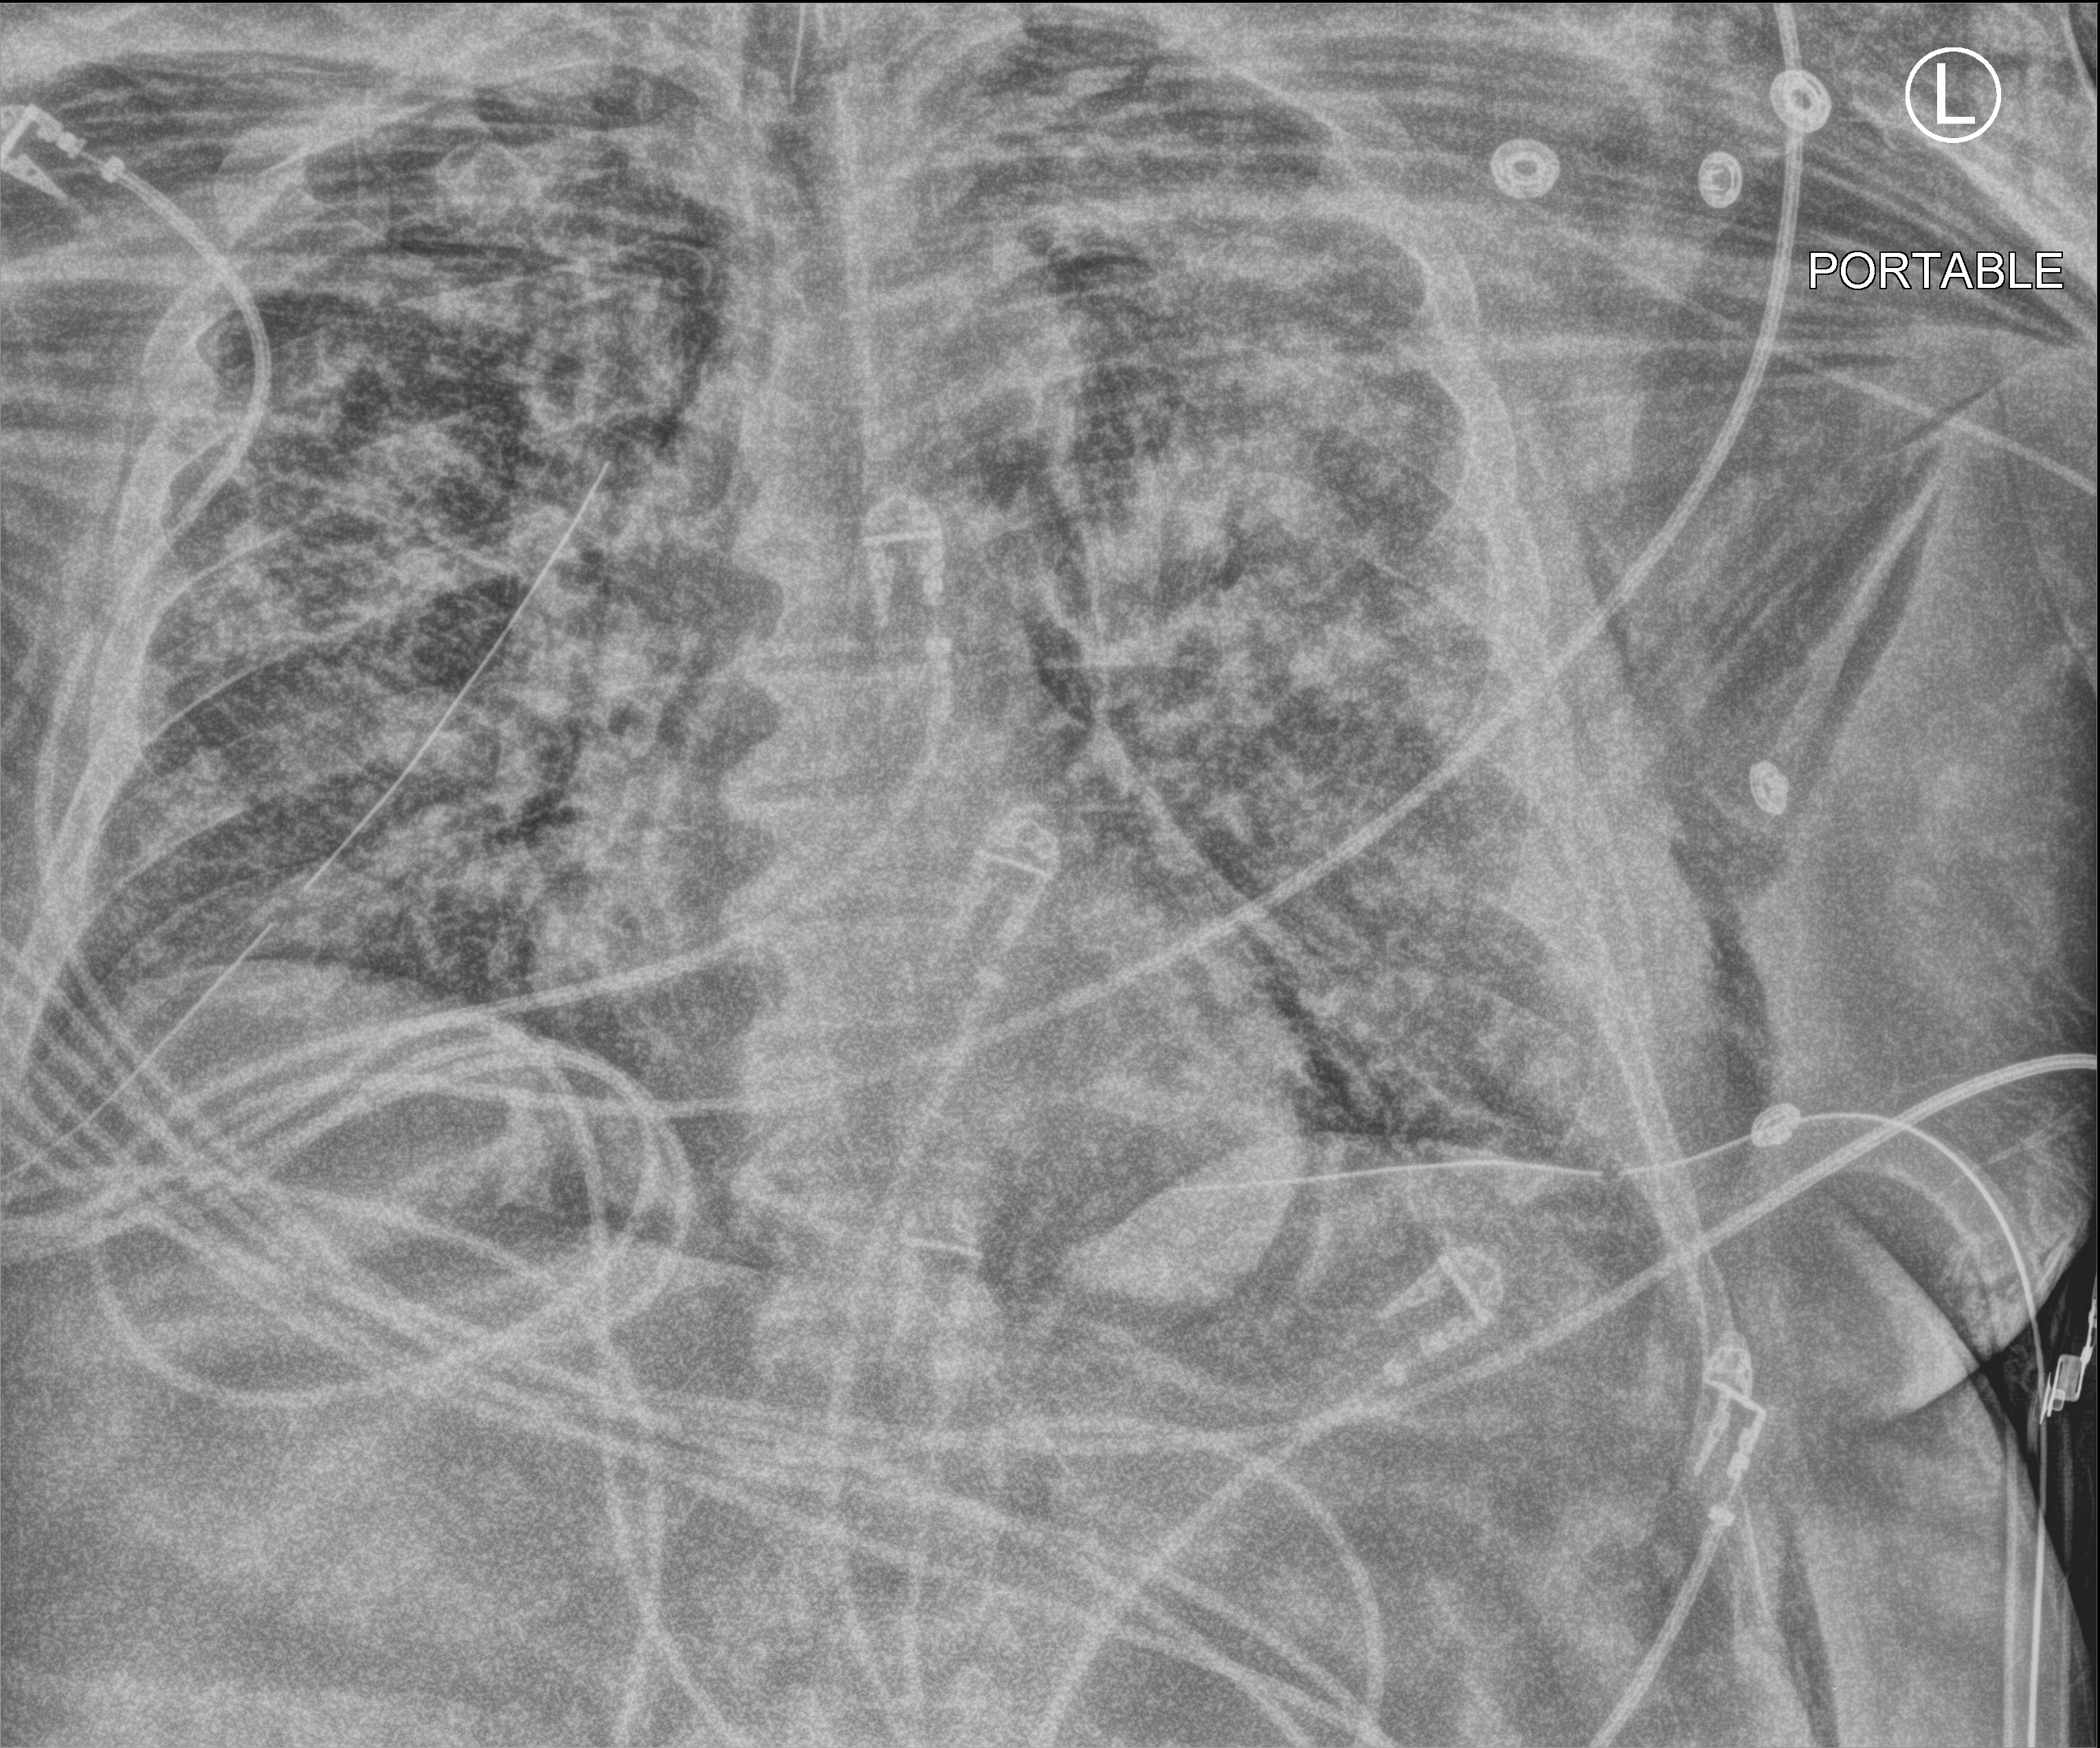
Portable chest radiograph; anteroposterior (AP) projection. Adult patient hospitalised with COVID-19, age 18–59 years.
From the hospital-stay record, not from the radiograph (when in the stay this image was taken is not recorded):
- mechanically ventilated during this hospital stay: yes
- length of hospital stay: 28 days